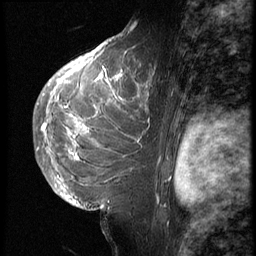
Breast MRI (dynamic contrast-enhanced), one sagittal slice; position 38 of 62 along the scan axis; 3 images stored at this slice position (order not interpretable as contrast timing); 1.5 T; TE 4.2 ms, TR 9 ms; 2.5 mm slice thickness; 256 × 256 image matrix, field of view 180 × 180 mm. Female patient, age 28 years. Case-level facts recorded for this patient, not image findings: setting: breast cancer imaged before/during neoadjuvant chemotherapy.
Structures marked on this image (semi-automatically segmented with operator editing):
- analysis volume of interest (the breast-tissue region the enhancement analysis was run in; not a lesion): bounding box <42,45,160,207> (left, top, right, bottom; pixels)
- tumour enhancement mask (voxels above the 140 % enhancement threshold inside the analysis volume of interest): <42,50,141,159>